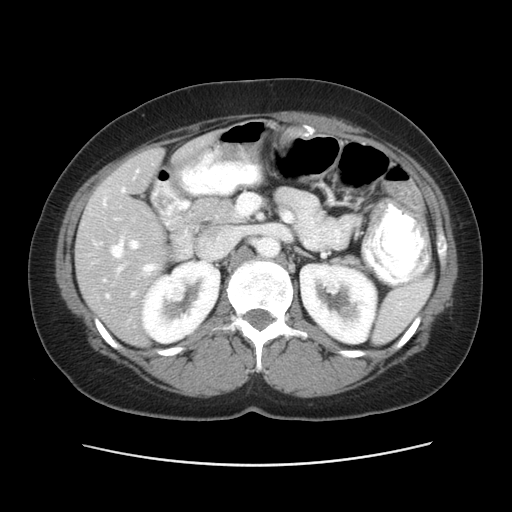
Contrast-enhanced abdominal CT, one axial slice. Slice 28 of 52 in the series (ordered by position). Reconstruction kernel STANDARD. 120 kVp. Intravenous contrast given. Soft-tissue window (W 400 / L 40 HU). 512 × 512 image matrix. Female patient, age 48 years. Case-level facts recorded for this patient, not image findings: diagnosis: colorectal cancer liver metastases, imaged before liver resection.
Outlined on this slice (outlined manually by an expert reader):
- hepatic veins: bounding box <103,218,156,298> (left, top, right, bottom; pixels)
- liver: <77,140,206,344>
- planned liver remnant (the part of the liver to remain after resection): <181,138,209,156>
- portal vein (with intrahepatic branches): <122,170,139,249>